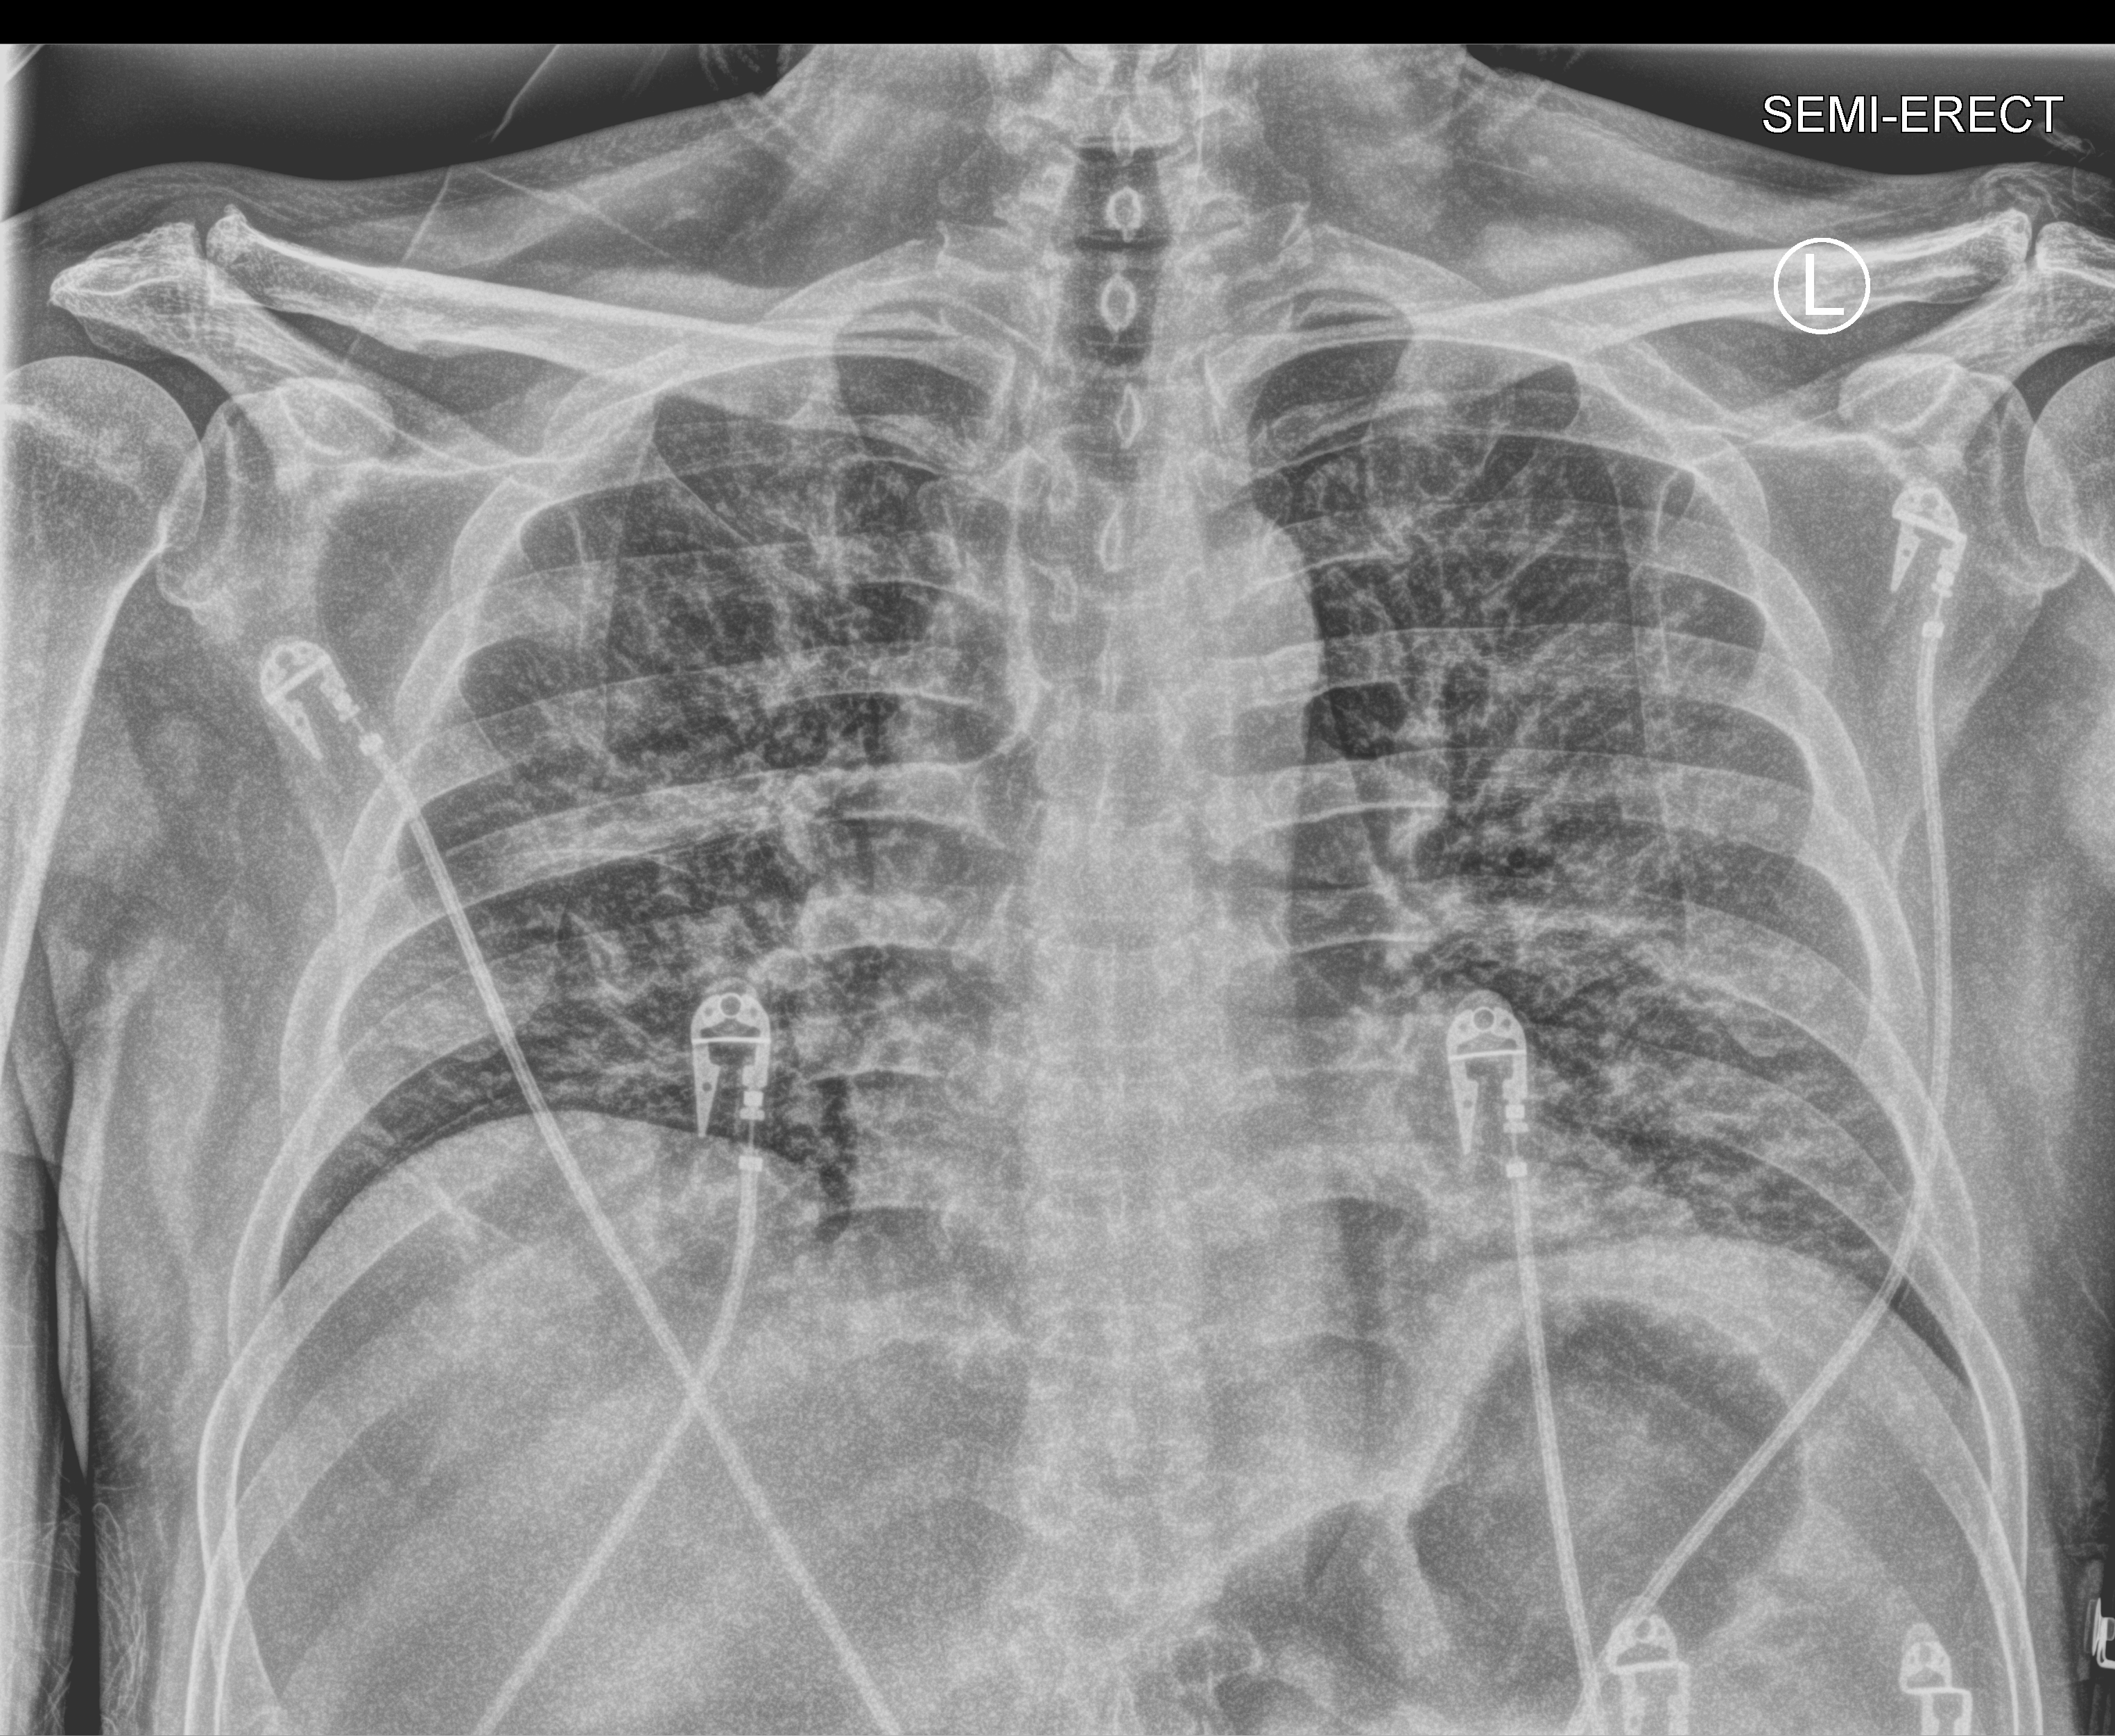
Chest X-ray (portable), anteroposterior (AP) projection. Male patient hospitalised with COVID-19, age 18–59 years.
Admission-level facts for this patient (not findings on this image; timing relative to this image not recorded): mechanically ventilated during this hospital stay: yes; COPD (admission record): no; chronic kidney disease (admission record): no.